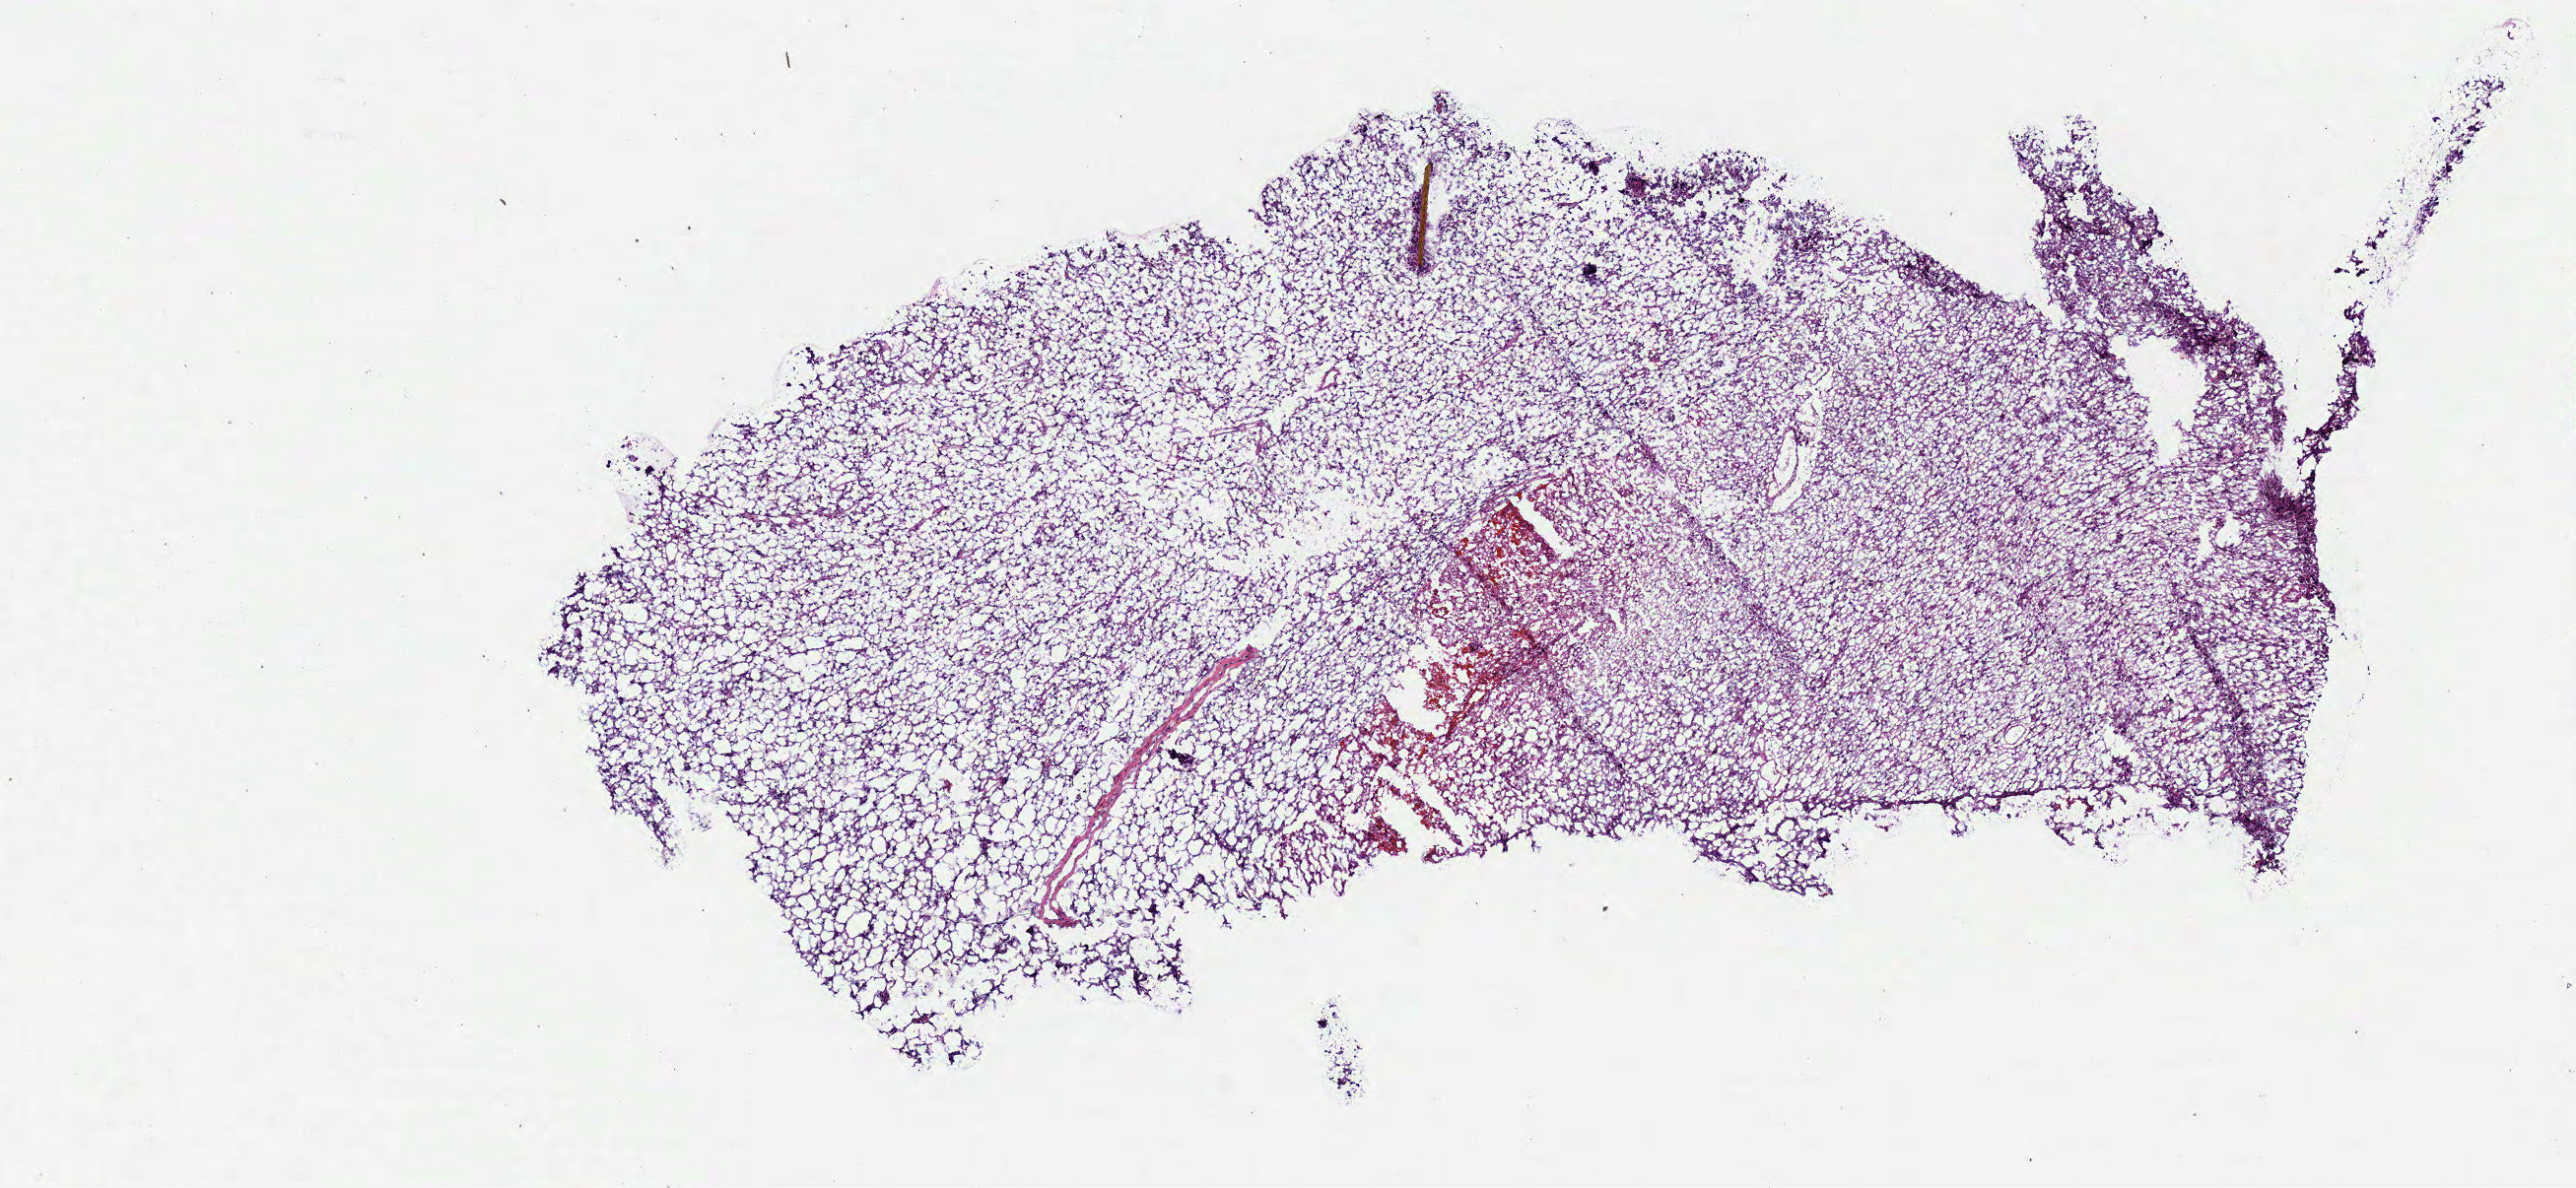
Digitized H&E tissue section (whole slide), a low-resolution overview of the entire scanned area, about 10.3 x 4.7 mm; frozen section; sample: primary tumour, brain. Female patient; age at initial diagnosis 31 years. Histologic grade: G2 (moderately differentiated). Pathologist review of this section (percent, as recorded): tumour cells 100%, tumour nuclei 80%, normal cells 0%, stromal cells 0%, necrosis 0%.
Diagnosis: Oligodendroglioma, NOS (cerebrum). Laterality: left.